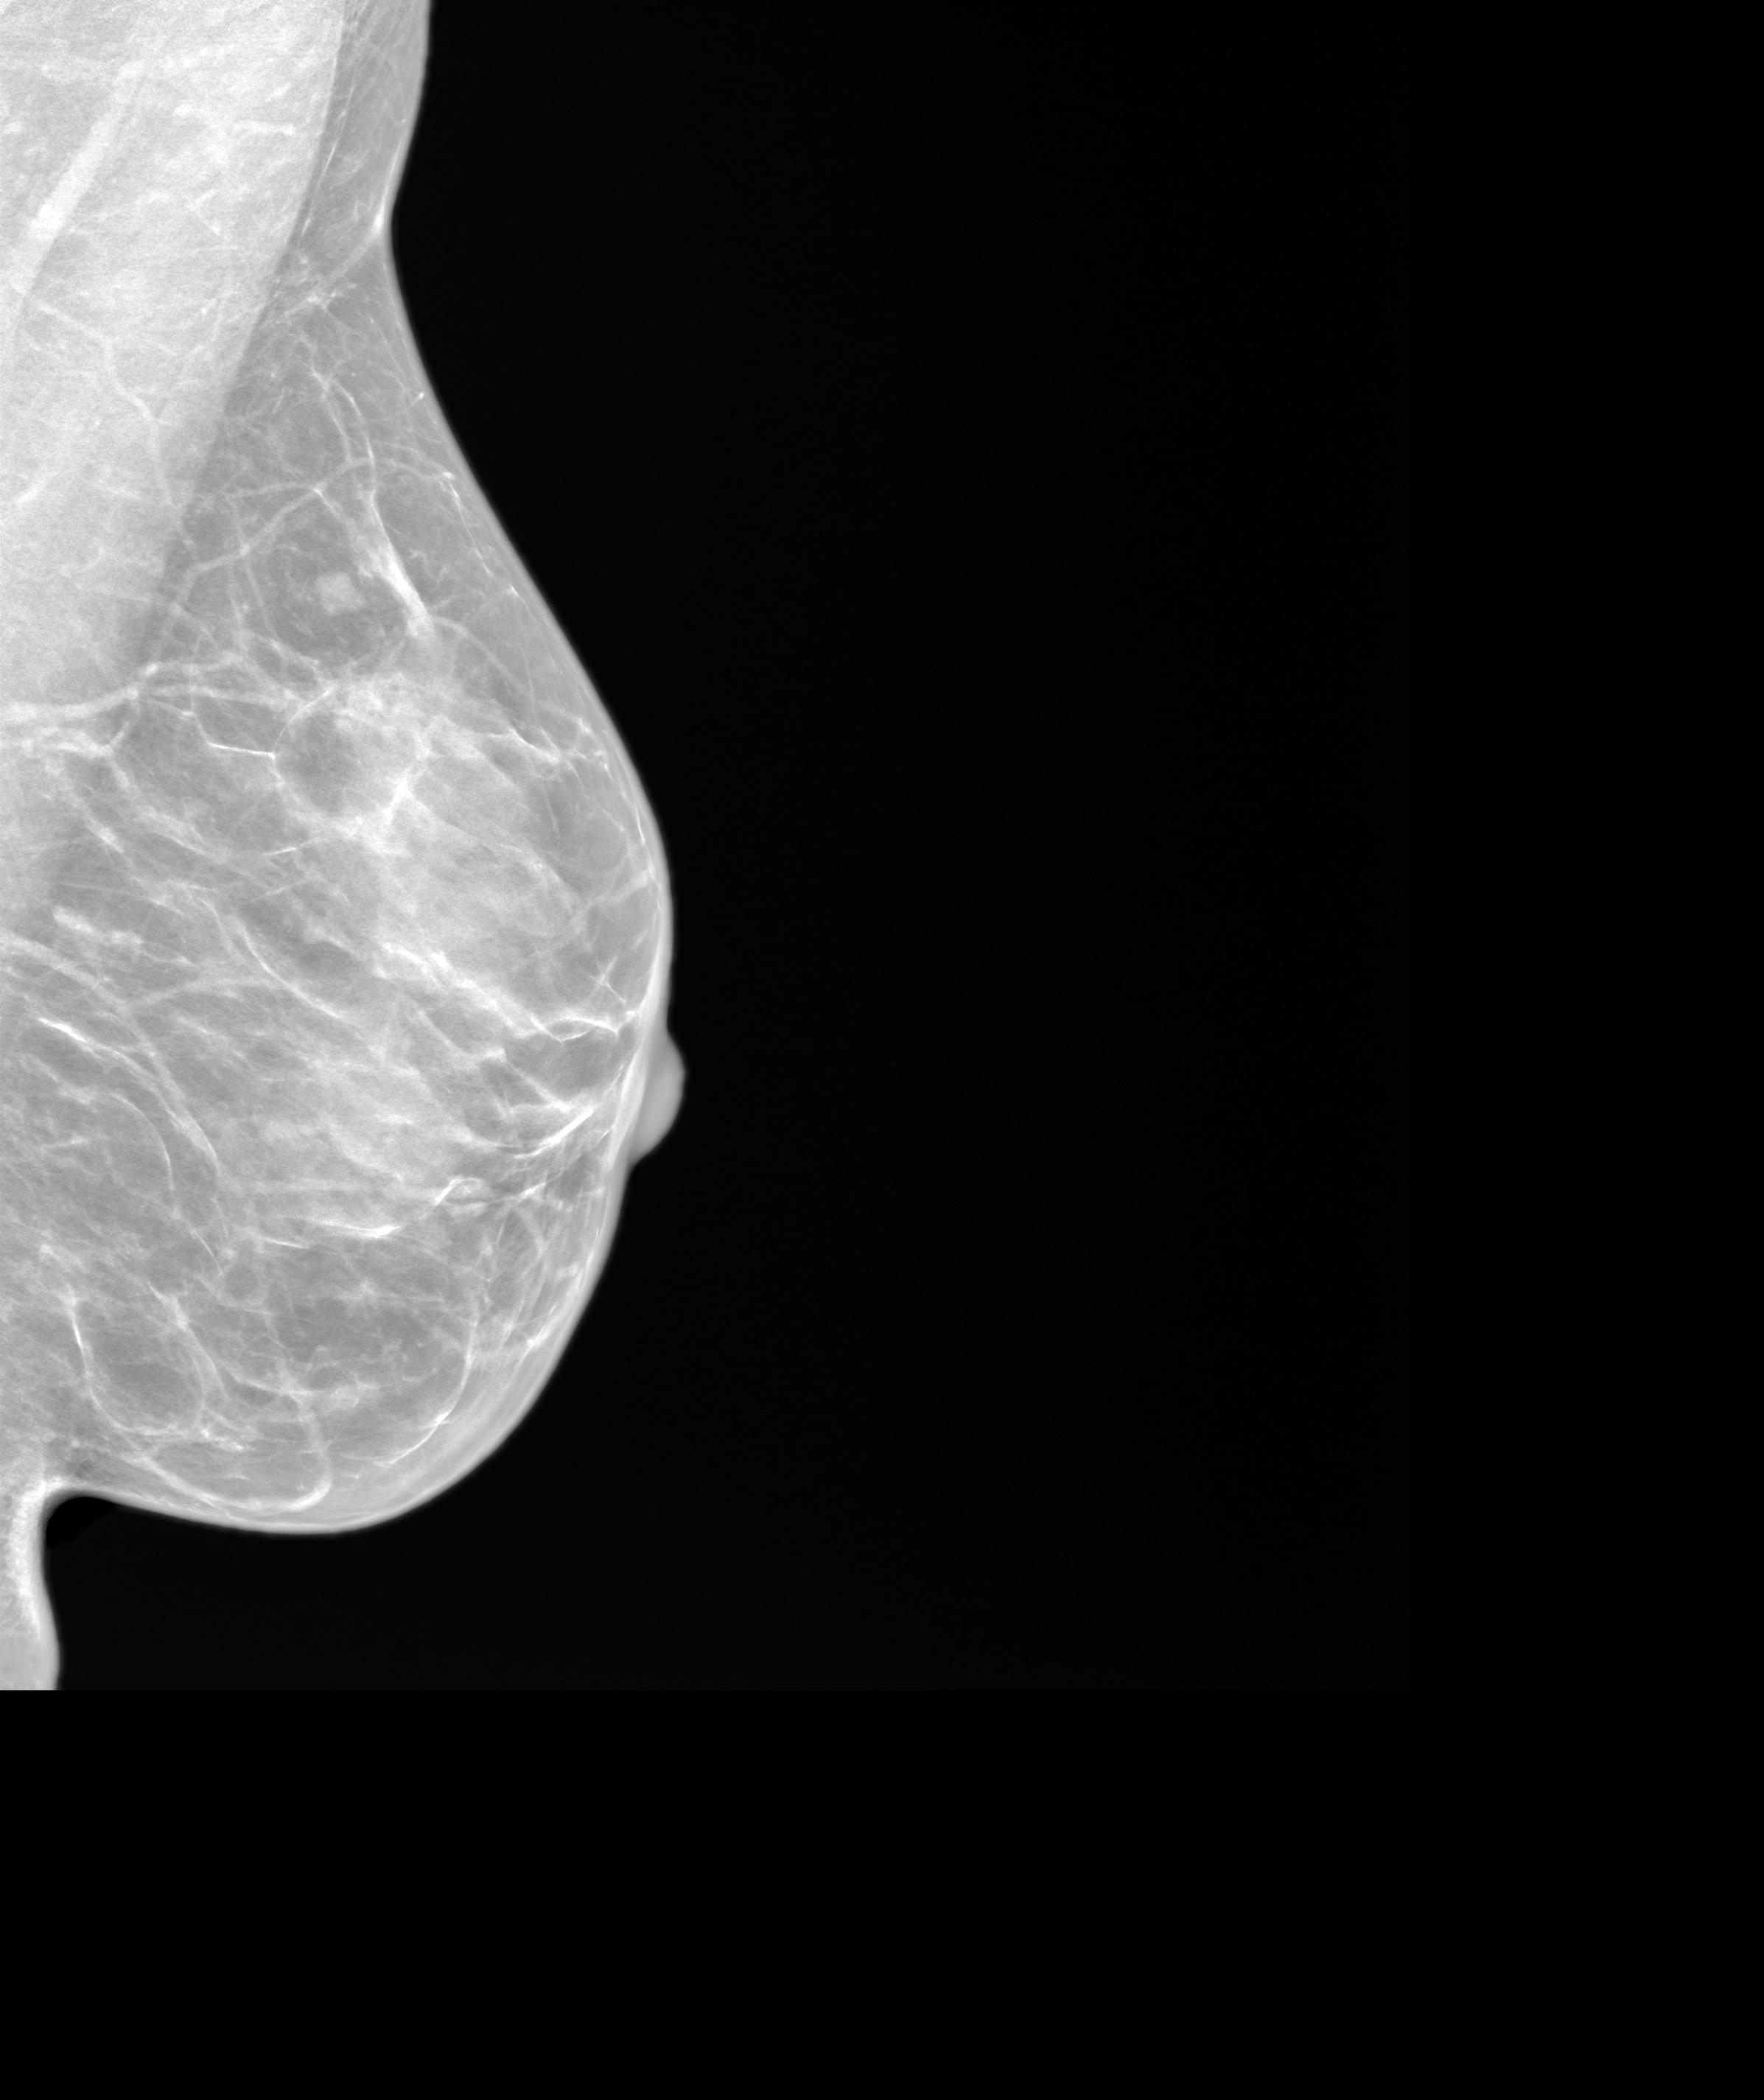
Screening examination, system: SenoIris_1SP1.2(425). Patient: female, 48 years.
Image type: synthesized 2-D view from tomosynthesis. Breast: left. Projection: mediolateral oblique (MLO) view.